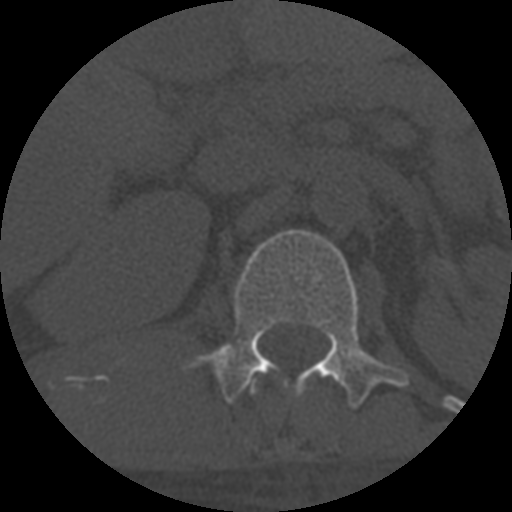
CT including the spine, one axial slice. Position 292 of 708 along the scan axis. Reconstruction kernel STANDARD. 120 kVp. One of 3 acquisitions stored at this slice position. Bone window (W 1800 / L 400 HU). 1.25 mm slice thickness. 512 × 512 image matrix, field of view 160 × 160 mm. Patient age 55 years. Case-level facts recorded for this patient, not image findings: primary cancer: colon; vertebrae with lytic lesions (as recorded): T12, L1, L5.
Annotated regions visible in this slice (semi-automatically segmented with operator editing):
- L1 vertebra: bounding box (x1, y1, x2, y2) in pixels: (182, 230, 409, 409)
- T12 vertebra: (247, 378, 257, 394)